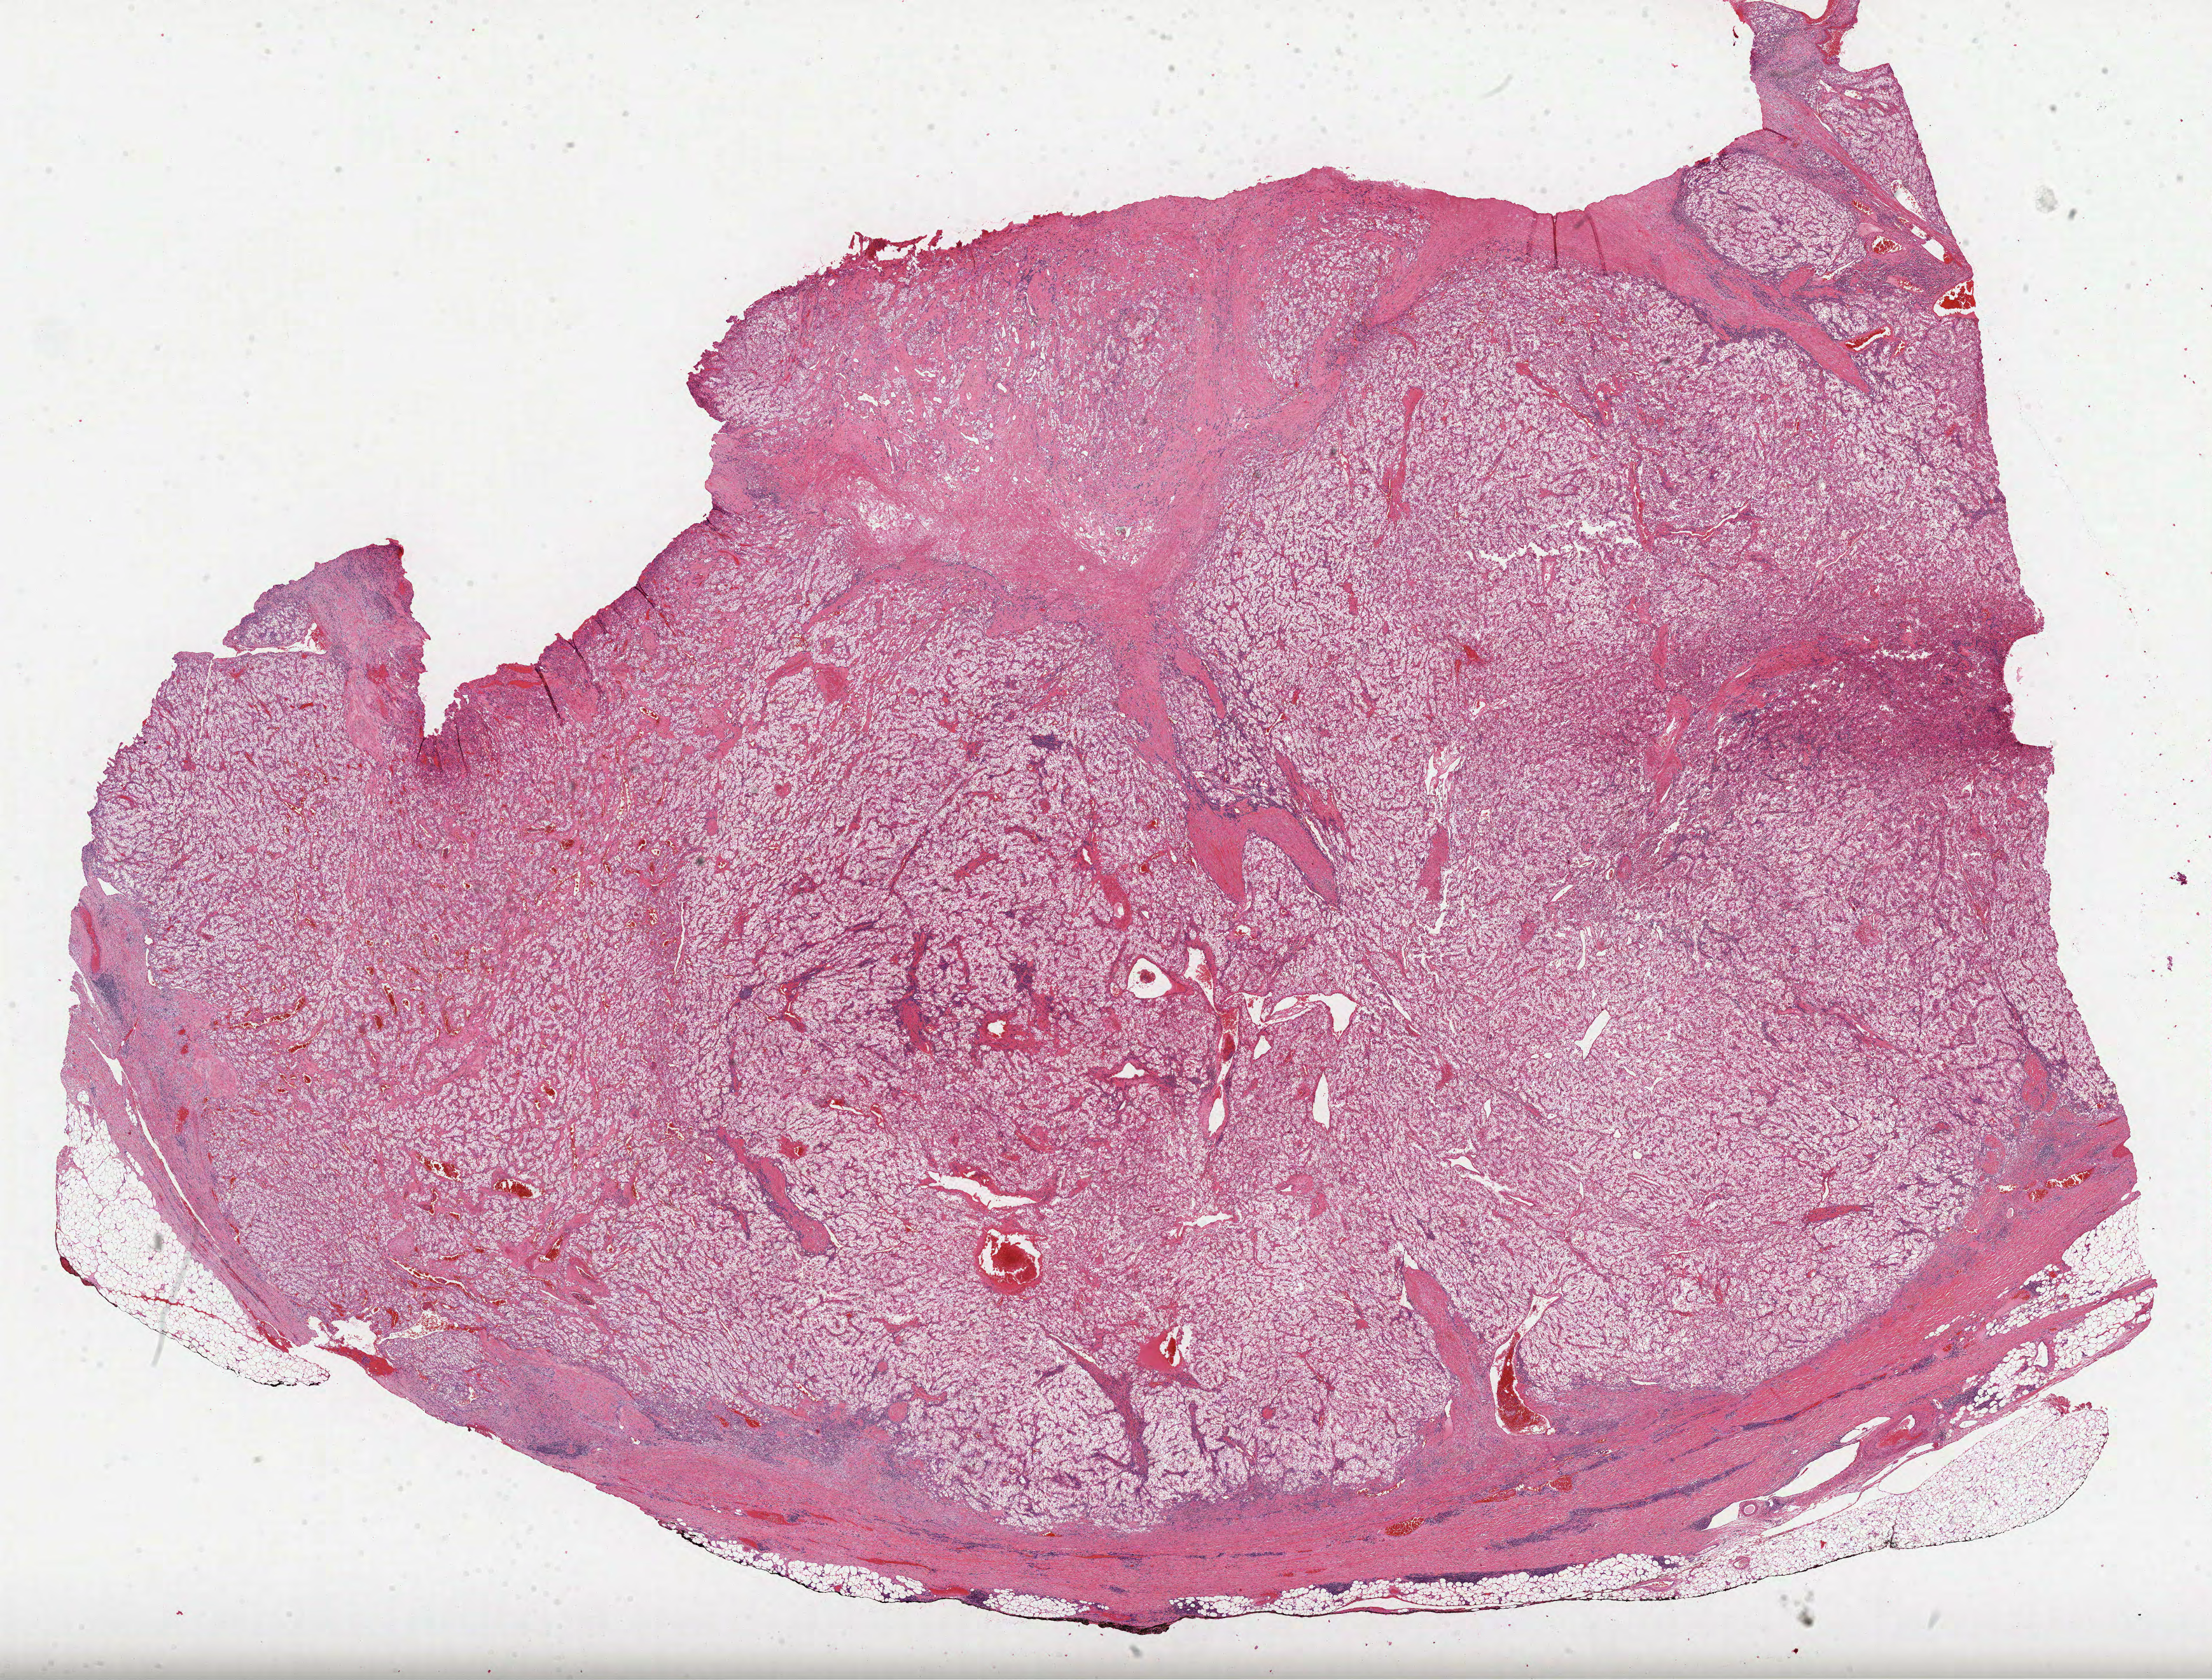
Whole-slide histology image, Hematoxylin and eosin (H&E) stained — a low-resolution overview of the entire scanned area, about 28.0 x 21.3 mm. FFPE section. Sample: primary tumour, kidney. Male patient; age at initial diagnosis 47 years.
Histologic diagnosis: Clear cell adenocarcinoma, NOS.